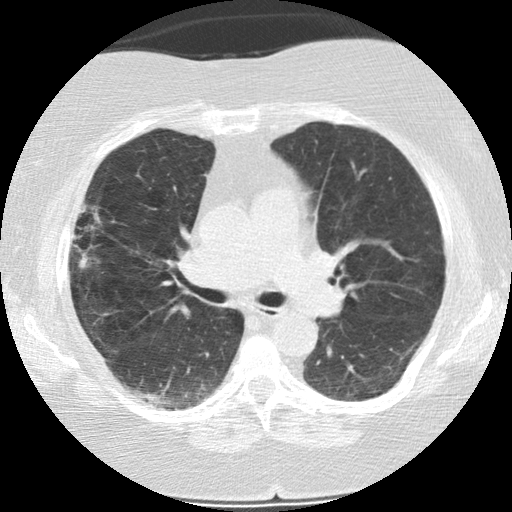
Low-dose screening chest CT, axial slice; baseline screening round; lung window (W 1500 / L -600 HU); slice 79 of 187 in the series; 512 × 512 image matrix. Female participant, aged 73 years at enrolment. Former smoker at enrolment.
Expert reader's lesion annotation, bounding box <58,215,116,278> (left, top, right, bottom; pixels). The exam's reader record, not a measurement of the box and not confirmed to be the same lesion: non-calcified nodule or mass ≥4 mm, right upper lobe, 21 × 14 mm, poorly defined margins, soft tissue attenuation.